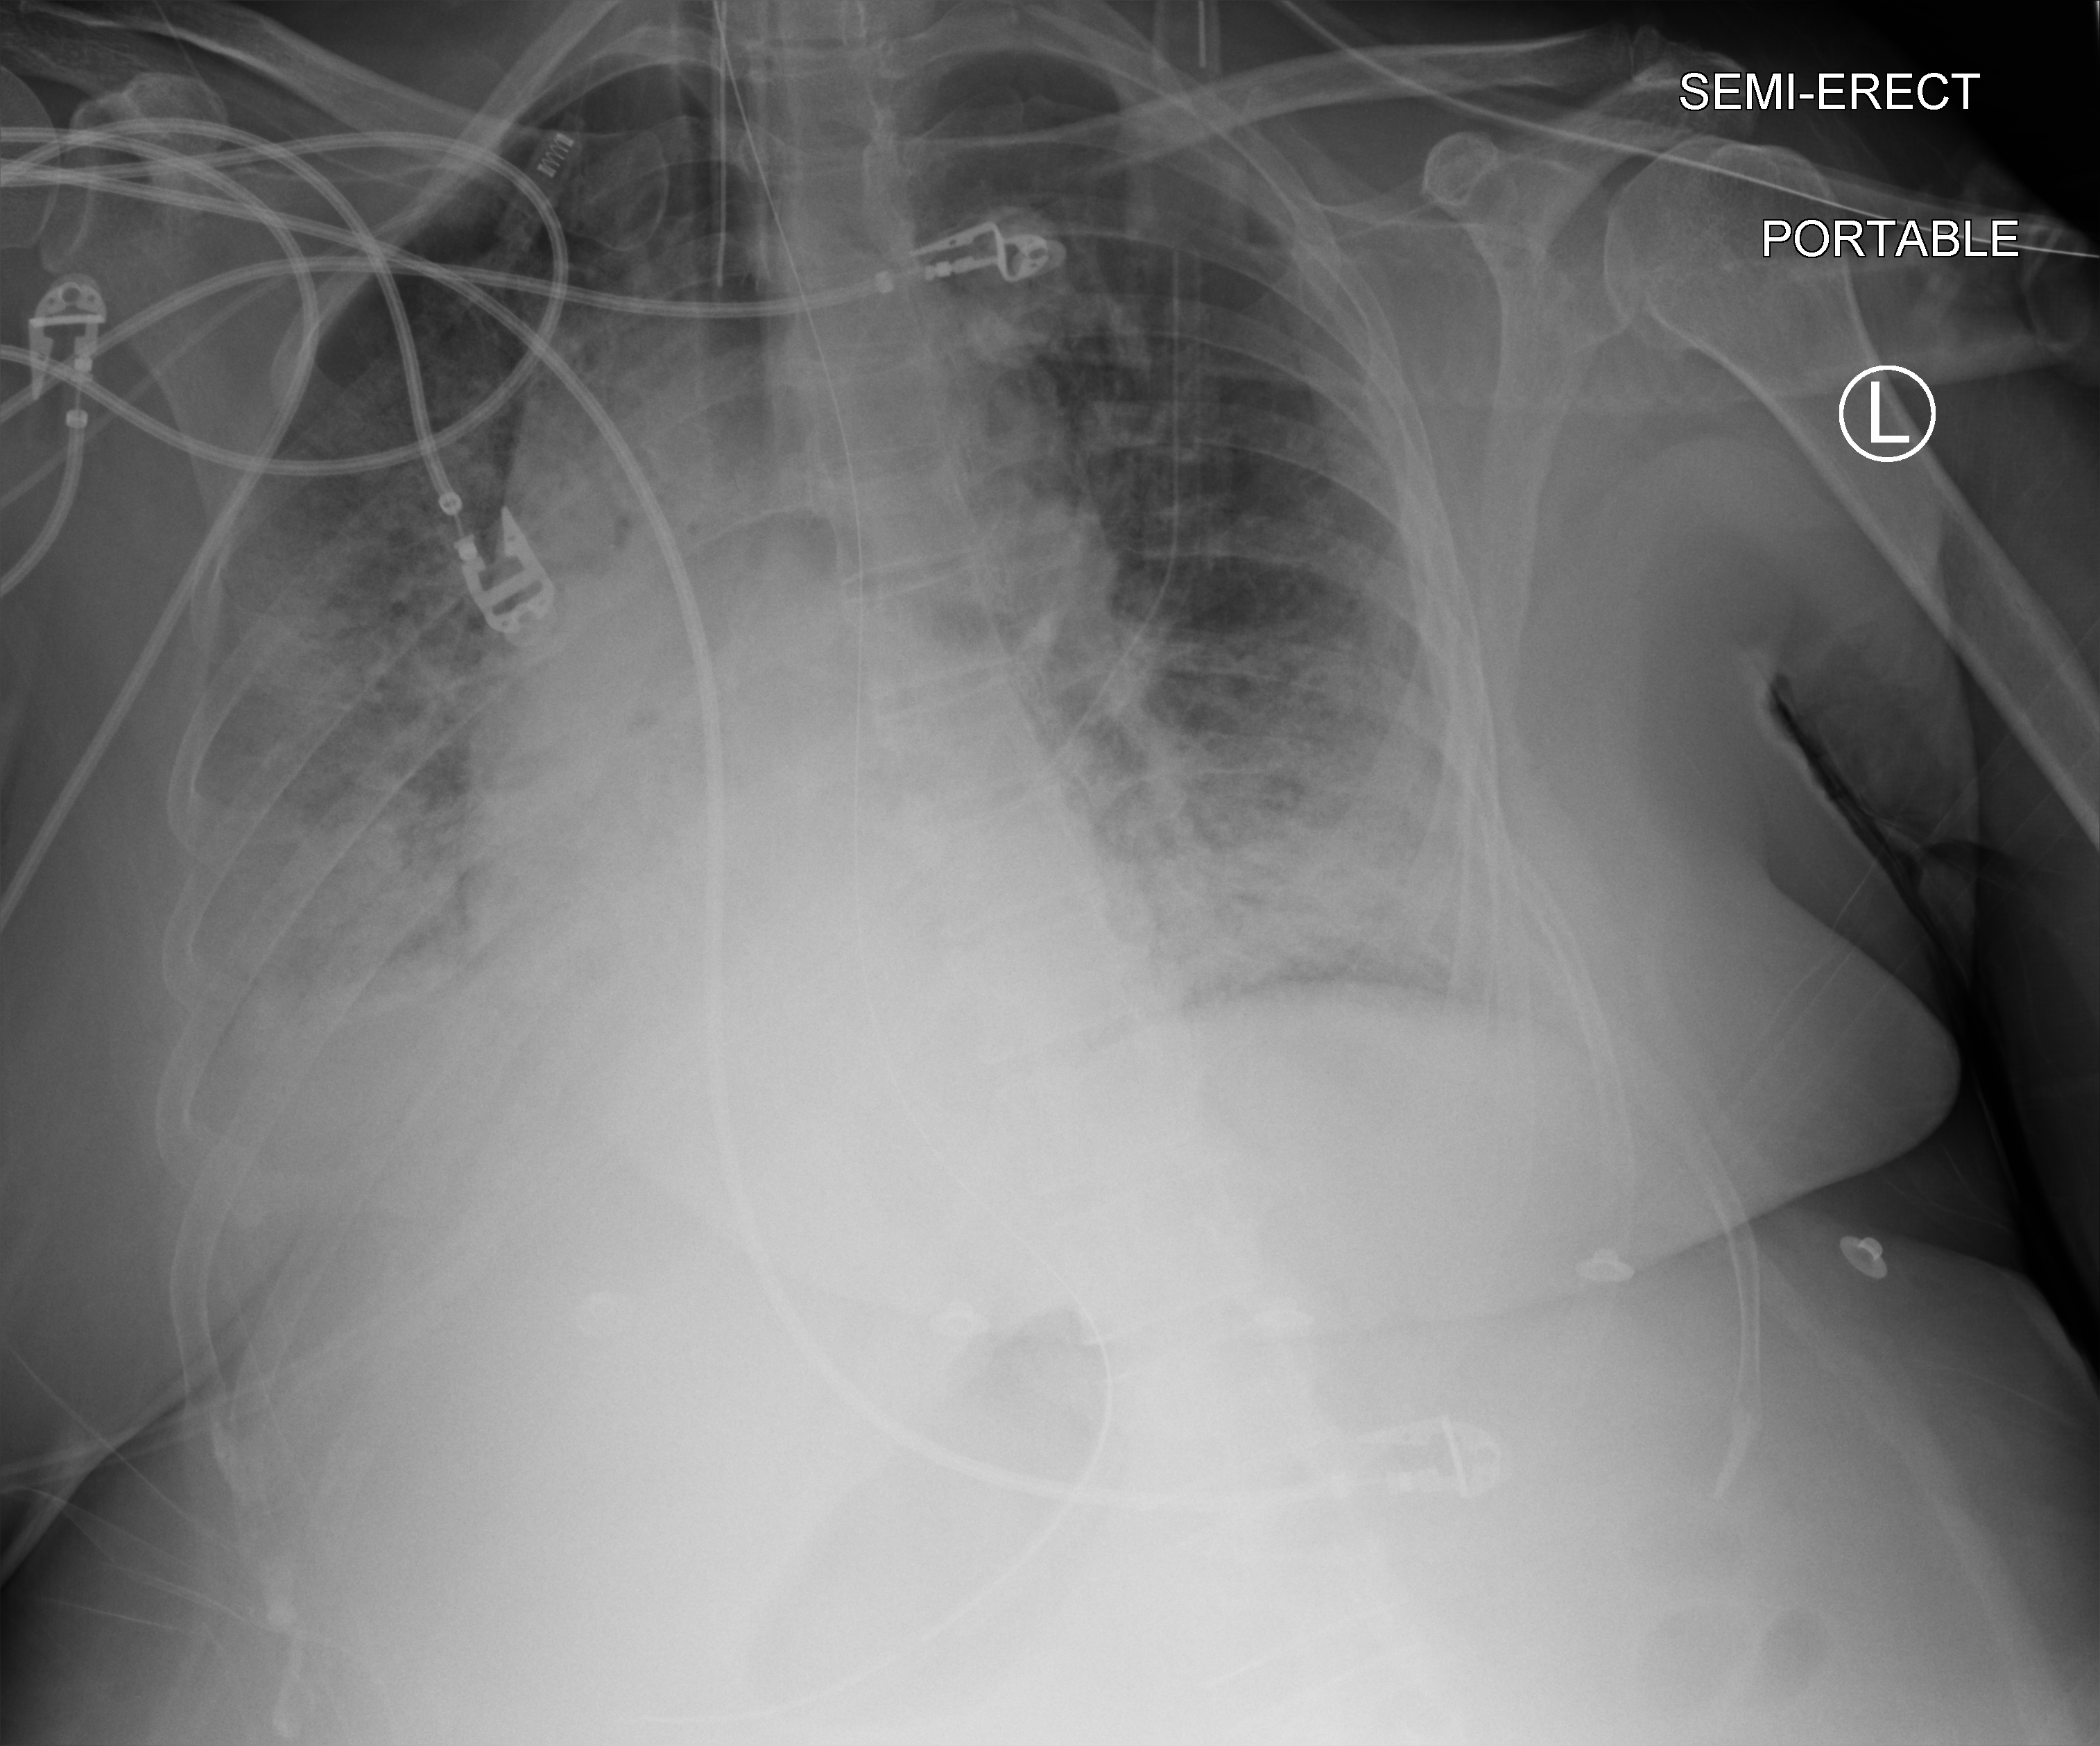
Bedside chest radiograph (computed radiography); anteroposterior (AP) projection. Female patient hospitalised with COVID-19, age 18–59 years.
From the hospital-stay record, not from the radiograph (when in the stay this image was taken is not recorded):
- admitted to intensive care during this hospital stay: yes